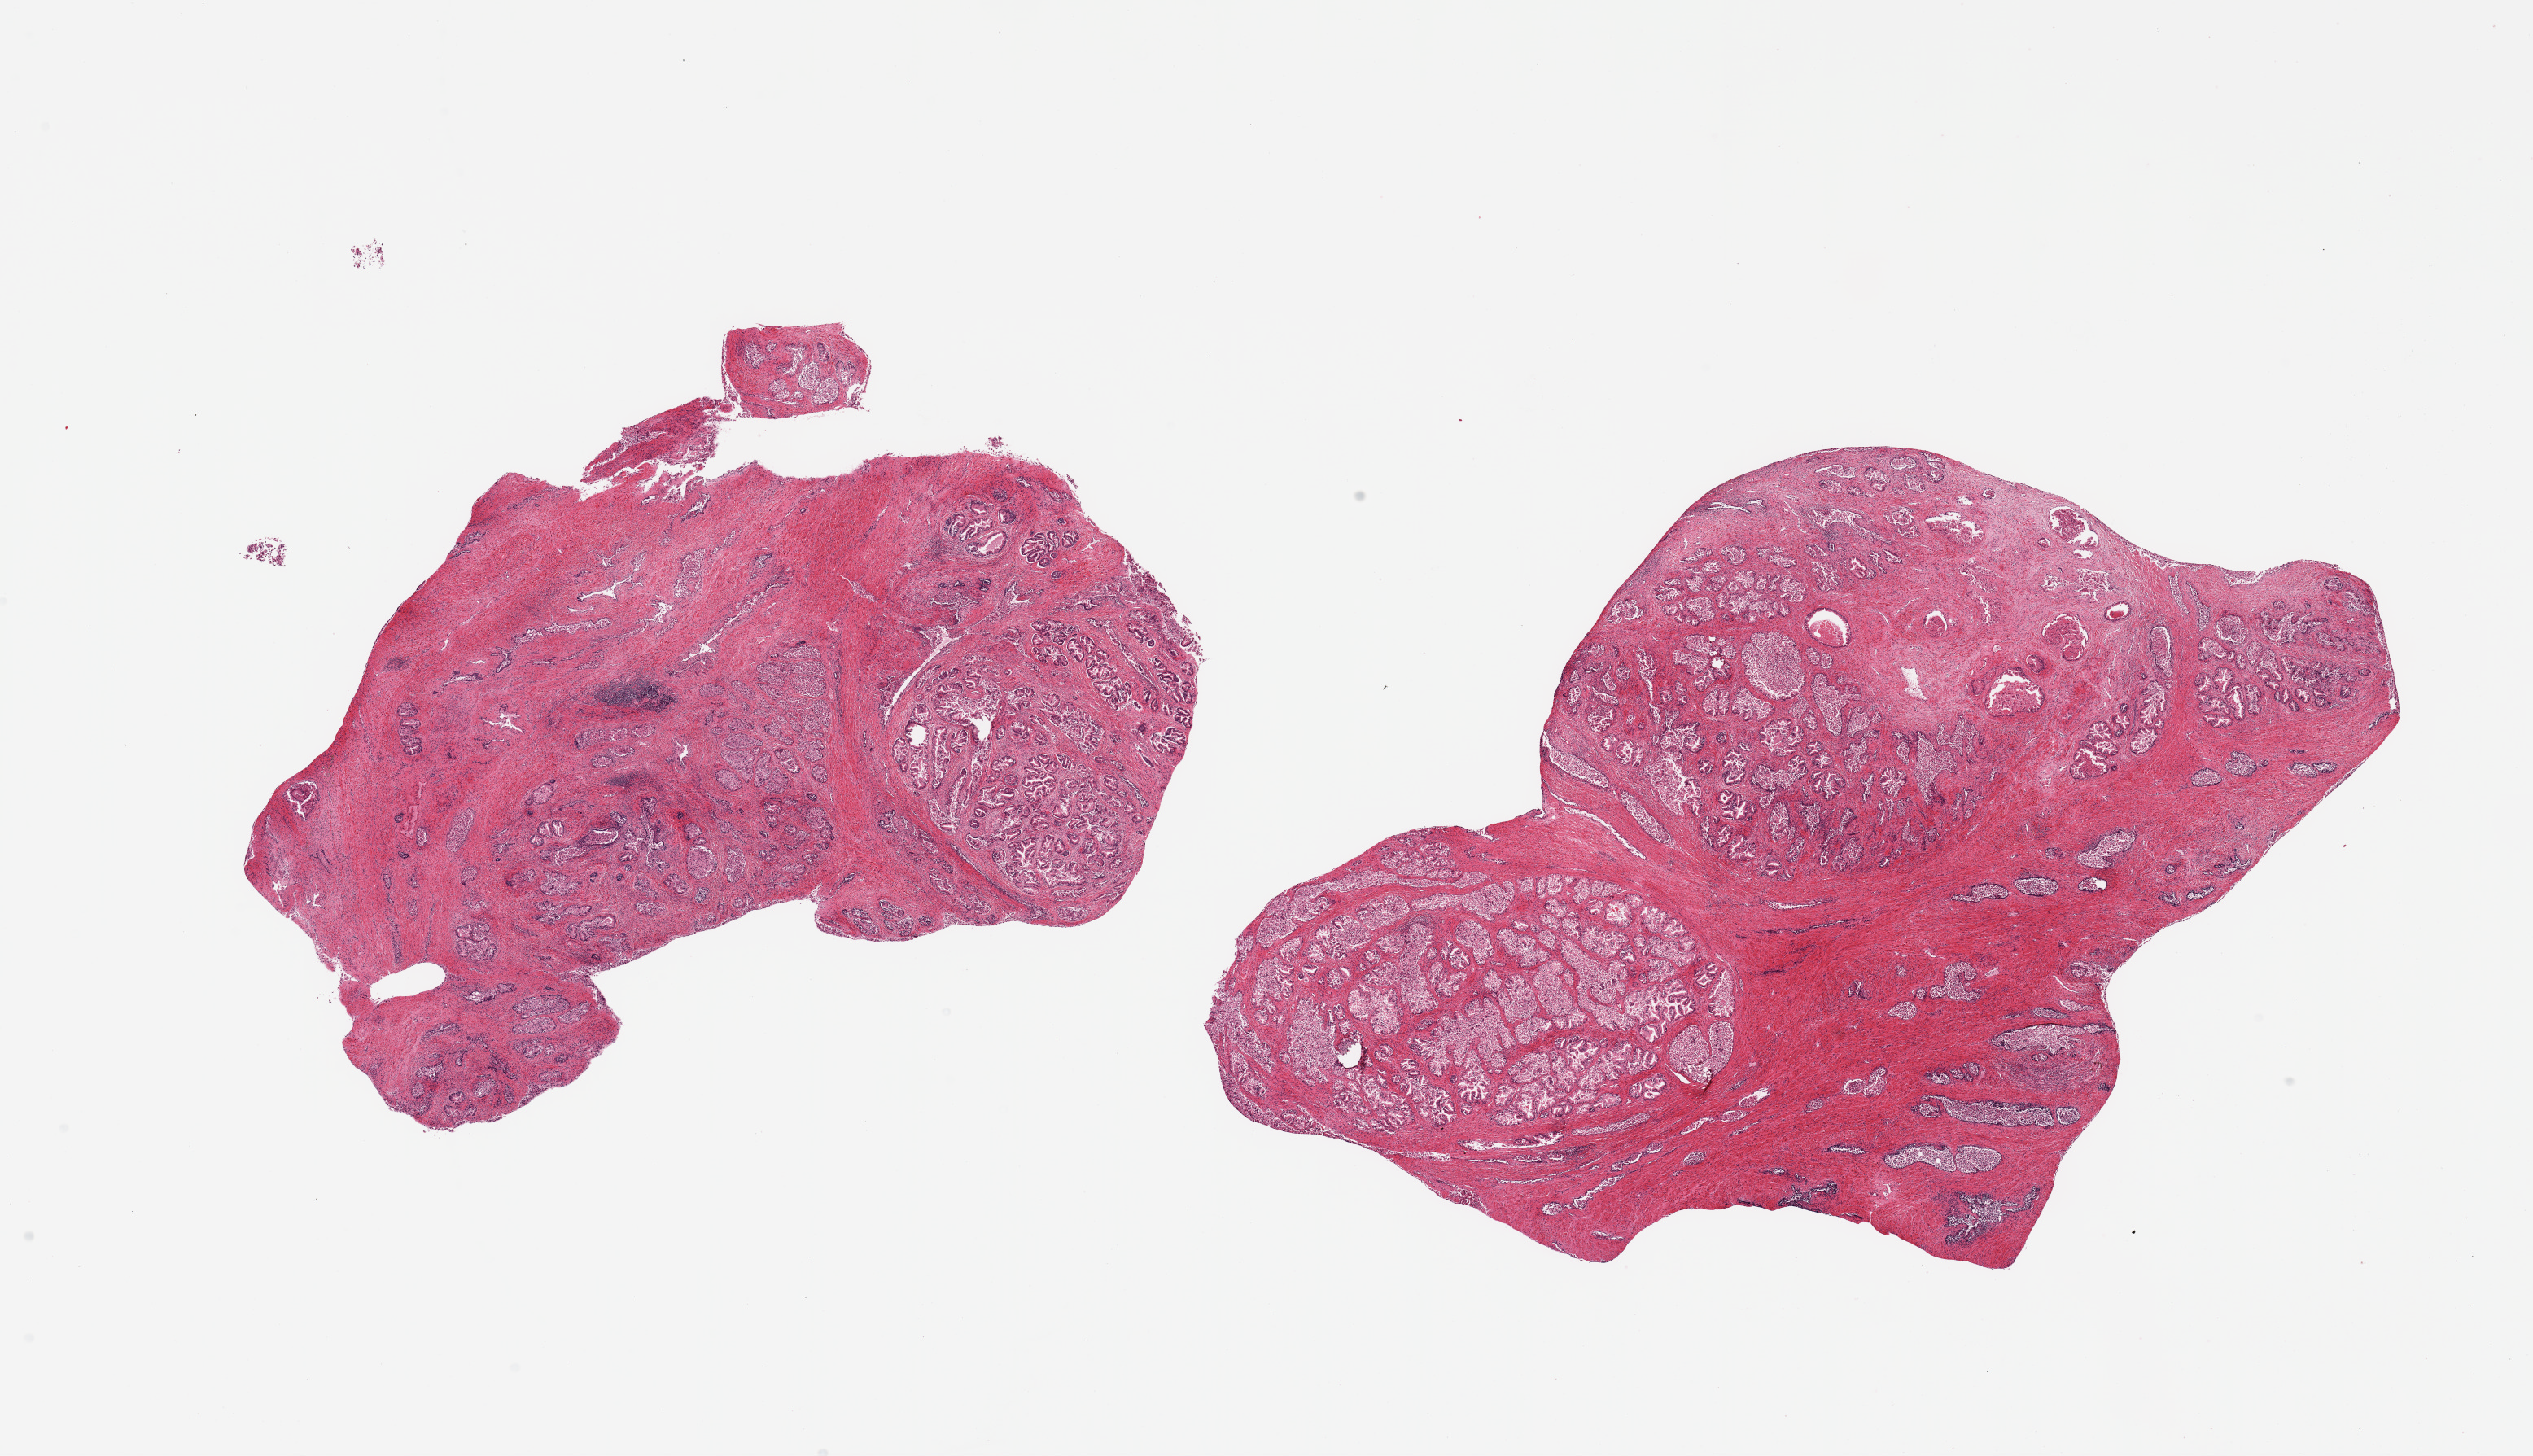
Digitized H&E-stained section, brightfield — low-resolution overview of the scanned area, about 24.6 x 14.1 mm (from a 20x scan); PAXgene-fixed paraffin-embedded (PFPE) section; sampled site (target tissue): prostate; tissue donor sample. Male donor.
• pathologist's review note for this sample: 2 pieces; nodular glandular hyperplasia; glands have moderate to severe autolysis